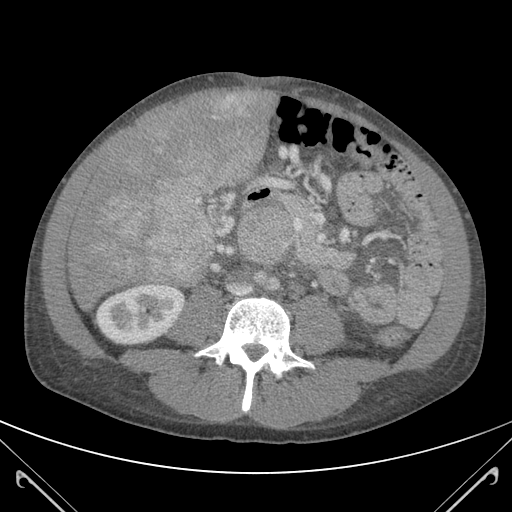
Contrast-enhanced abdominal CT (liver protocol), one axial slice; soft-tissue window (W 400 / L 40 HU); 3 mm slice thickness; 512 × 512 image matrix, field of view 380 × 380 mm. From the clinical record (not read from this slice): diagnosis: hepatocellular carcinoma (patient treated with transarterial chemoembolisation; whether this scan precedes or follows treatment is not stated here); TNM stage (as recorded): Stage-IIIB; Child-Pugh class: A; tumour nodularity: uninodular.
Annotated regions visible in this slice (semi-automatic segmentation, software-assisted and operator-edited):
- mass: bounding box [x1, y1, x2, y2] px = [89, 91, 266, 285]